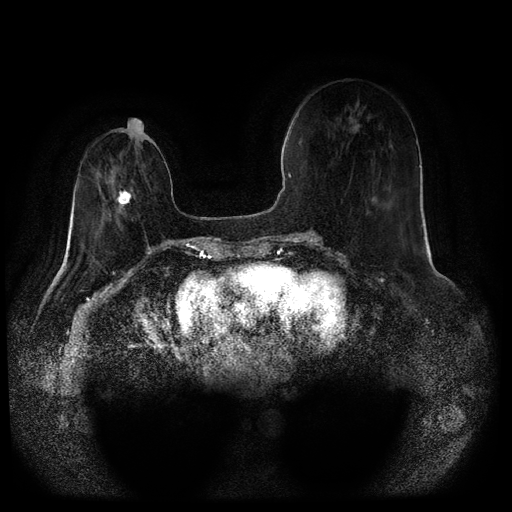
Breast MRI (dynamic contrast-enhanced, multi-phase), one axial slice; dynamic contrast-enhanced series, time point 2 of 5 at this slice position (early post-contrast); 1.5 T; TE 2.6 ms, TR 5.3 ms; 512 × 512 image matrix, field of view 360 × 360 mm. Female patient, age 71 years.
Annotated regions visible in this slice (semi-automatic segmentation, software-assisted and operator-edited):
- breast lesion (labelled 'tumour' in the annotation; benign lesions carry a separate 'benign' label): box from (x=114, y=187) to (x=134, y=207) px